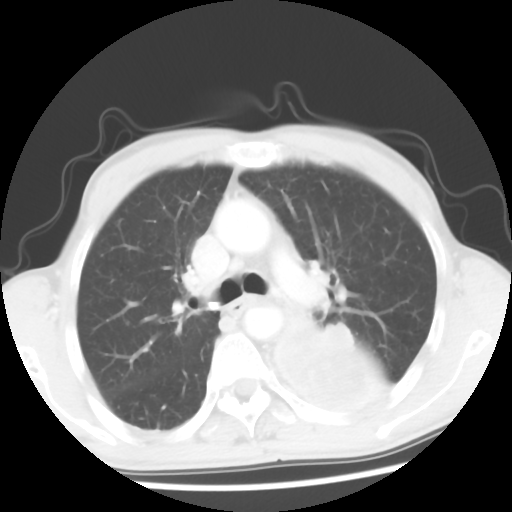
Chest CT, one axial slice; slice 38 of 56 in the series (ordered by position); lung window (W 1500 / L -600 HU); 512 × 512 image matrix, field of view 318 × 318 mm. Patient: male, 60 years. Case-level facts recorded for this patient, not image findings: clinical TNM (as recorded): T4 N0 M0.
Outlined on this slice (bounding box drawn by a radiologist):
- lung tumour (recorded histology: squamous cell carcinoma): bounding box [x1, y1, x2, y2] px = [264, 322, 391, 416]